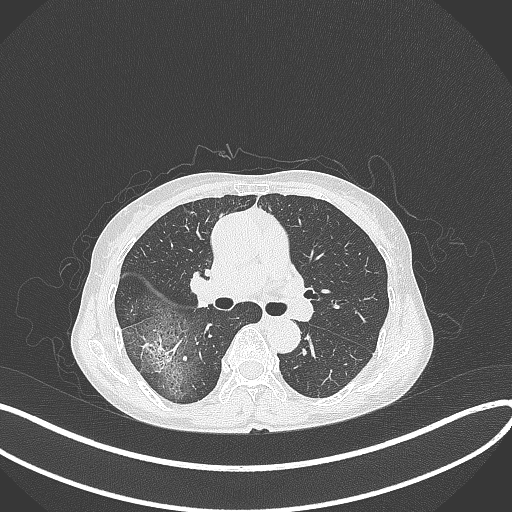
Chest CT, one axial slice; position 235 of 371 along the scan axis; reconstruction kernel B70f; lung window (W 1500 / L -600 HU); 512 × 512 image matrix. Patient: female, 69 years. From the clinical record (not read from this slice): clinical TNM (as recorded): T1b N0 M0; histopathological grade: G2-3.
Structures marked on this image (rectangle marked by the reading radiologist):
- lung tumour (recorded histology: adenocarcinoma): box from (x=135, y=328) to (x=183, y=375) px